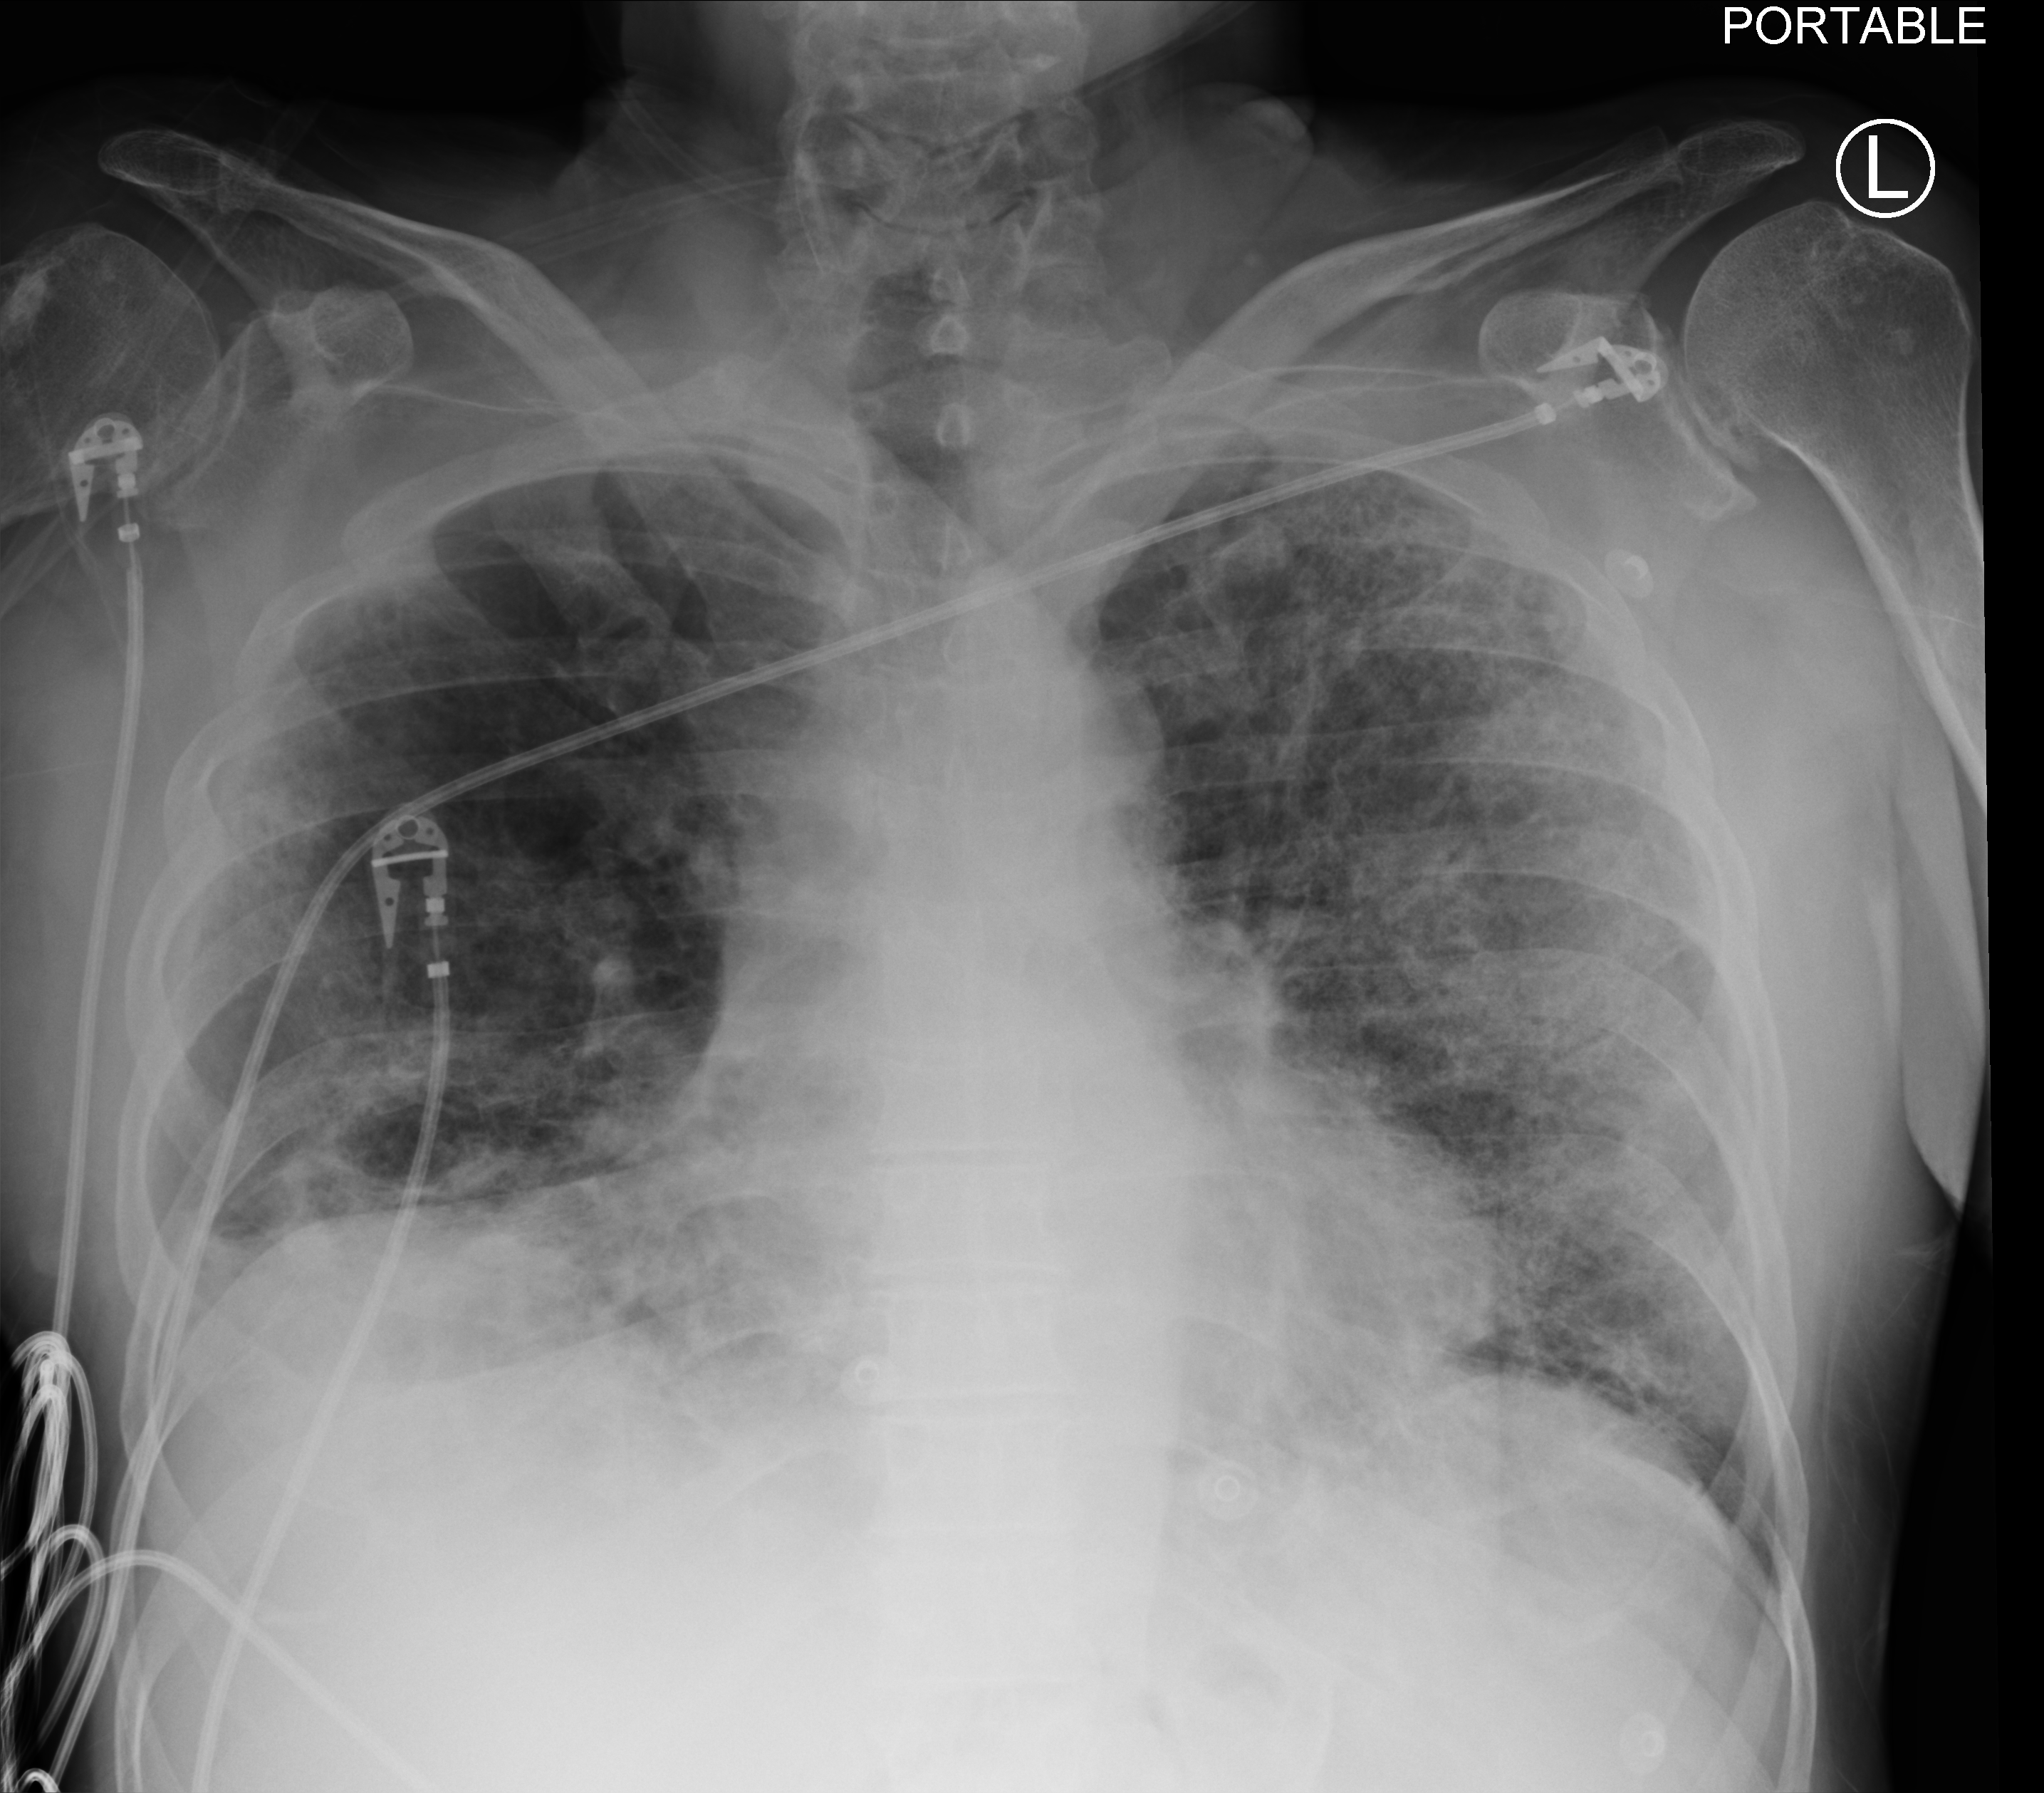
Chest X-ray (portable); anteroposterior (AP) projection. Male patient hospitalised with COVID-19, age 60–74 years.
Hospital-stay facts (about this admission, not read from this image; timing relative to this image not recorded): mechanically ventilated during this hospital stay: no.